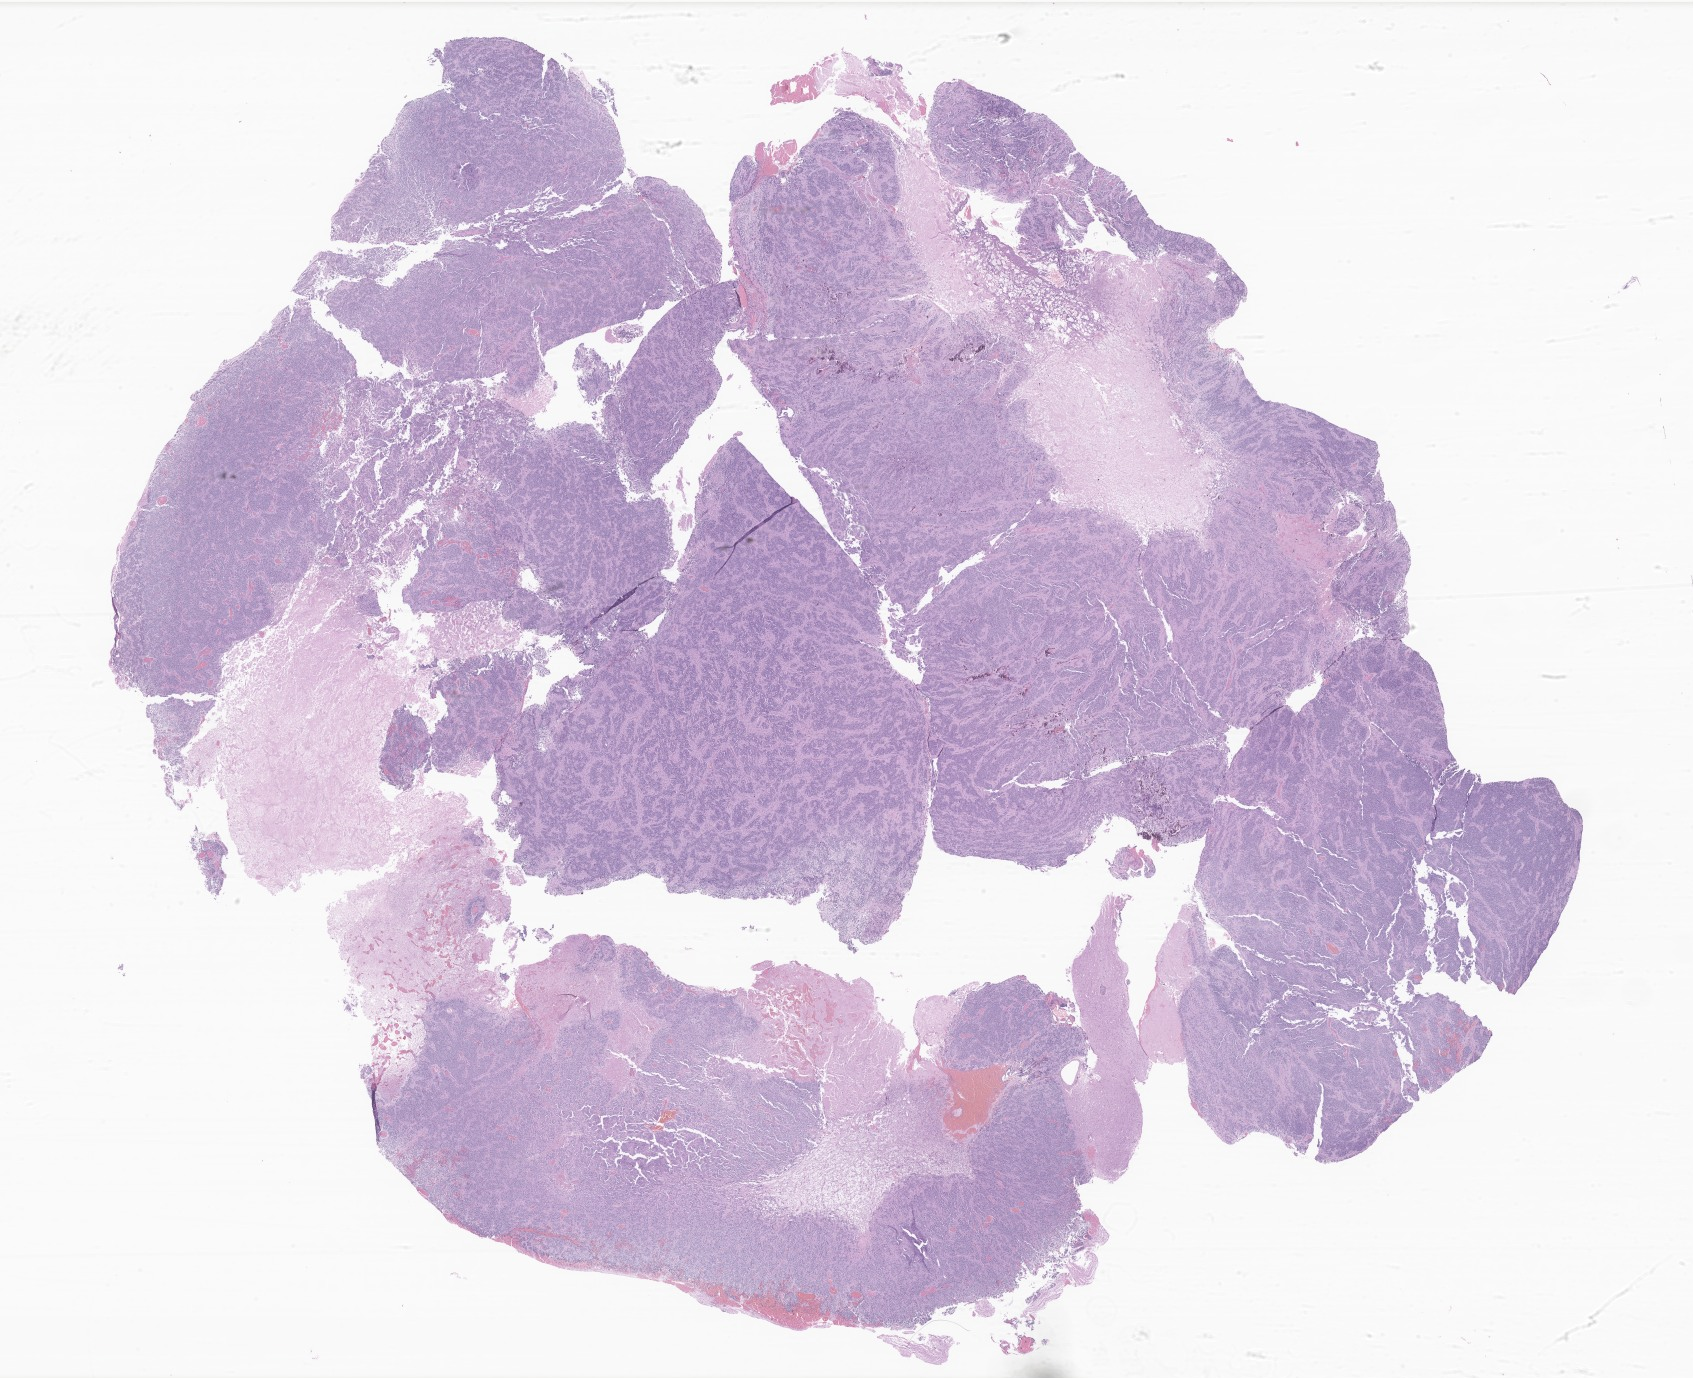
H&E whole-slide image of tumor tissue from the brain, low-resolution overview of the scanned area, about 28.6 x 23.2 mm, formalin-fixed paraffin-embedded section. Patient female; age 228 months (19 years).
Diagnosis: Ependymoma, NOS.